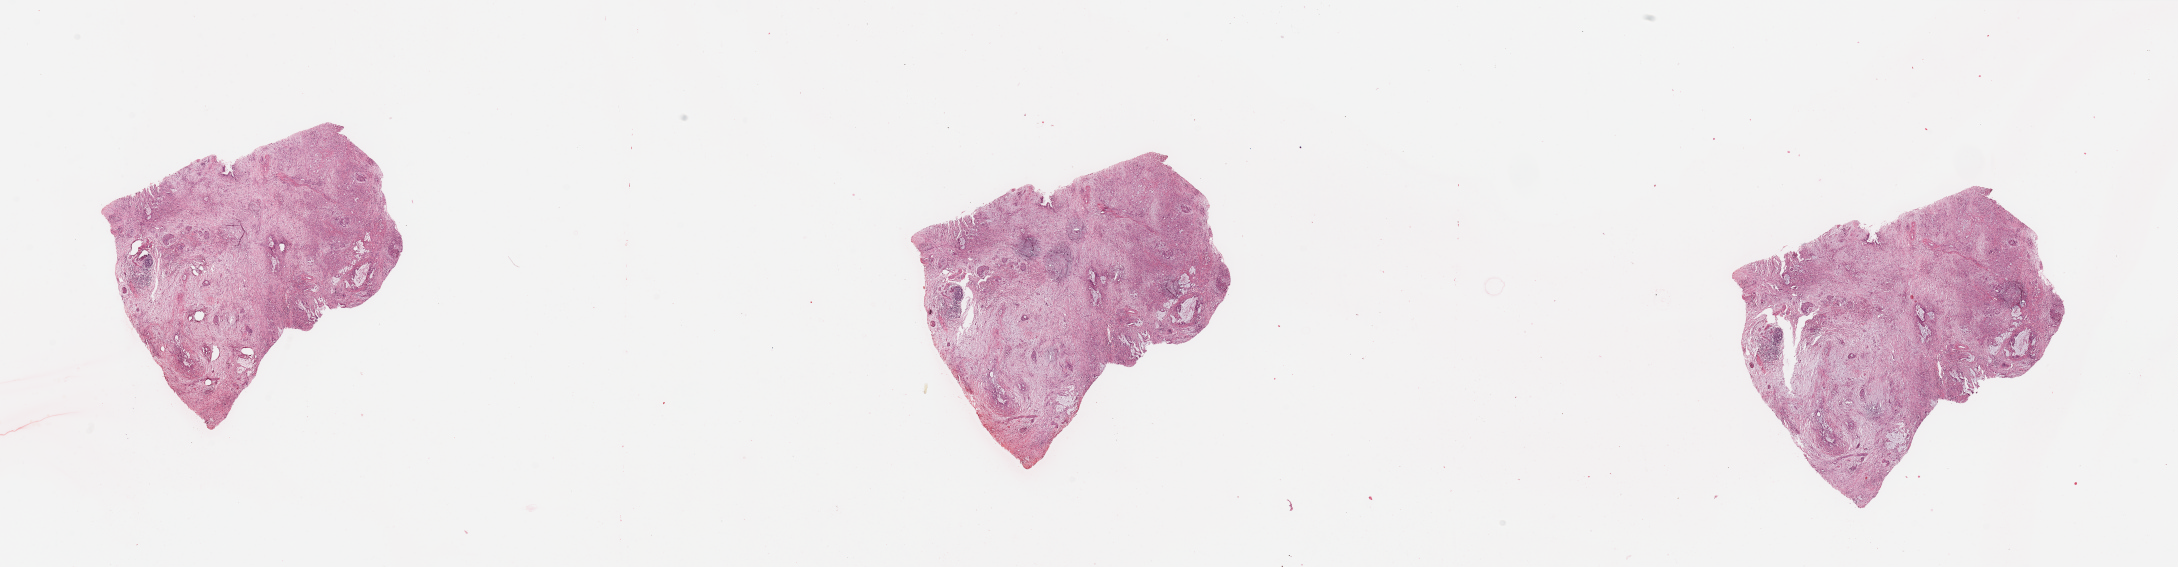
Digitized H&E tissue section (whole slide), a low-resolution overview of the entire scanned area, about 34.5 x 9.0 mm (acquisition: 20x scan), pancreas, tumour tissue. Patient: male, age 72 years. Histologic grade: G2 (moderately differentiated).
* diagnosis: Infiltrating duct carcinoma, NOS
* AJCC pathologic stage: IB